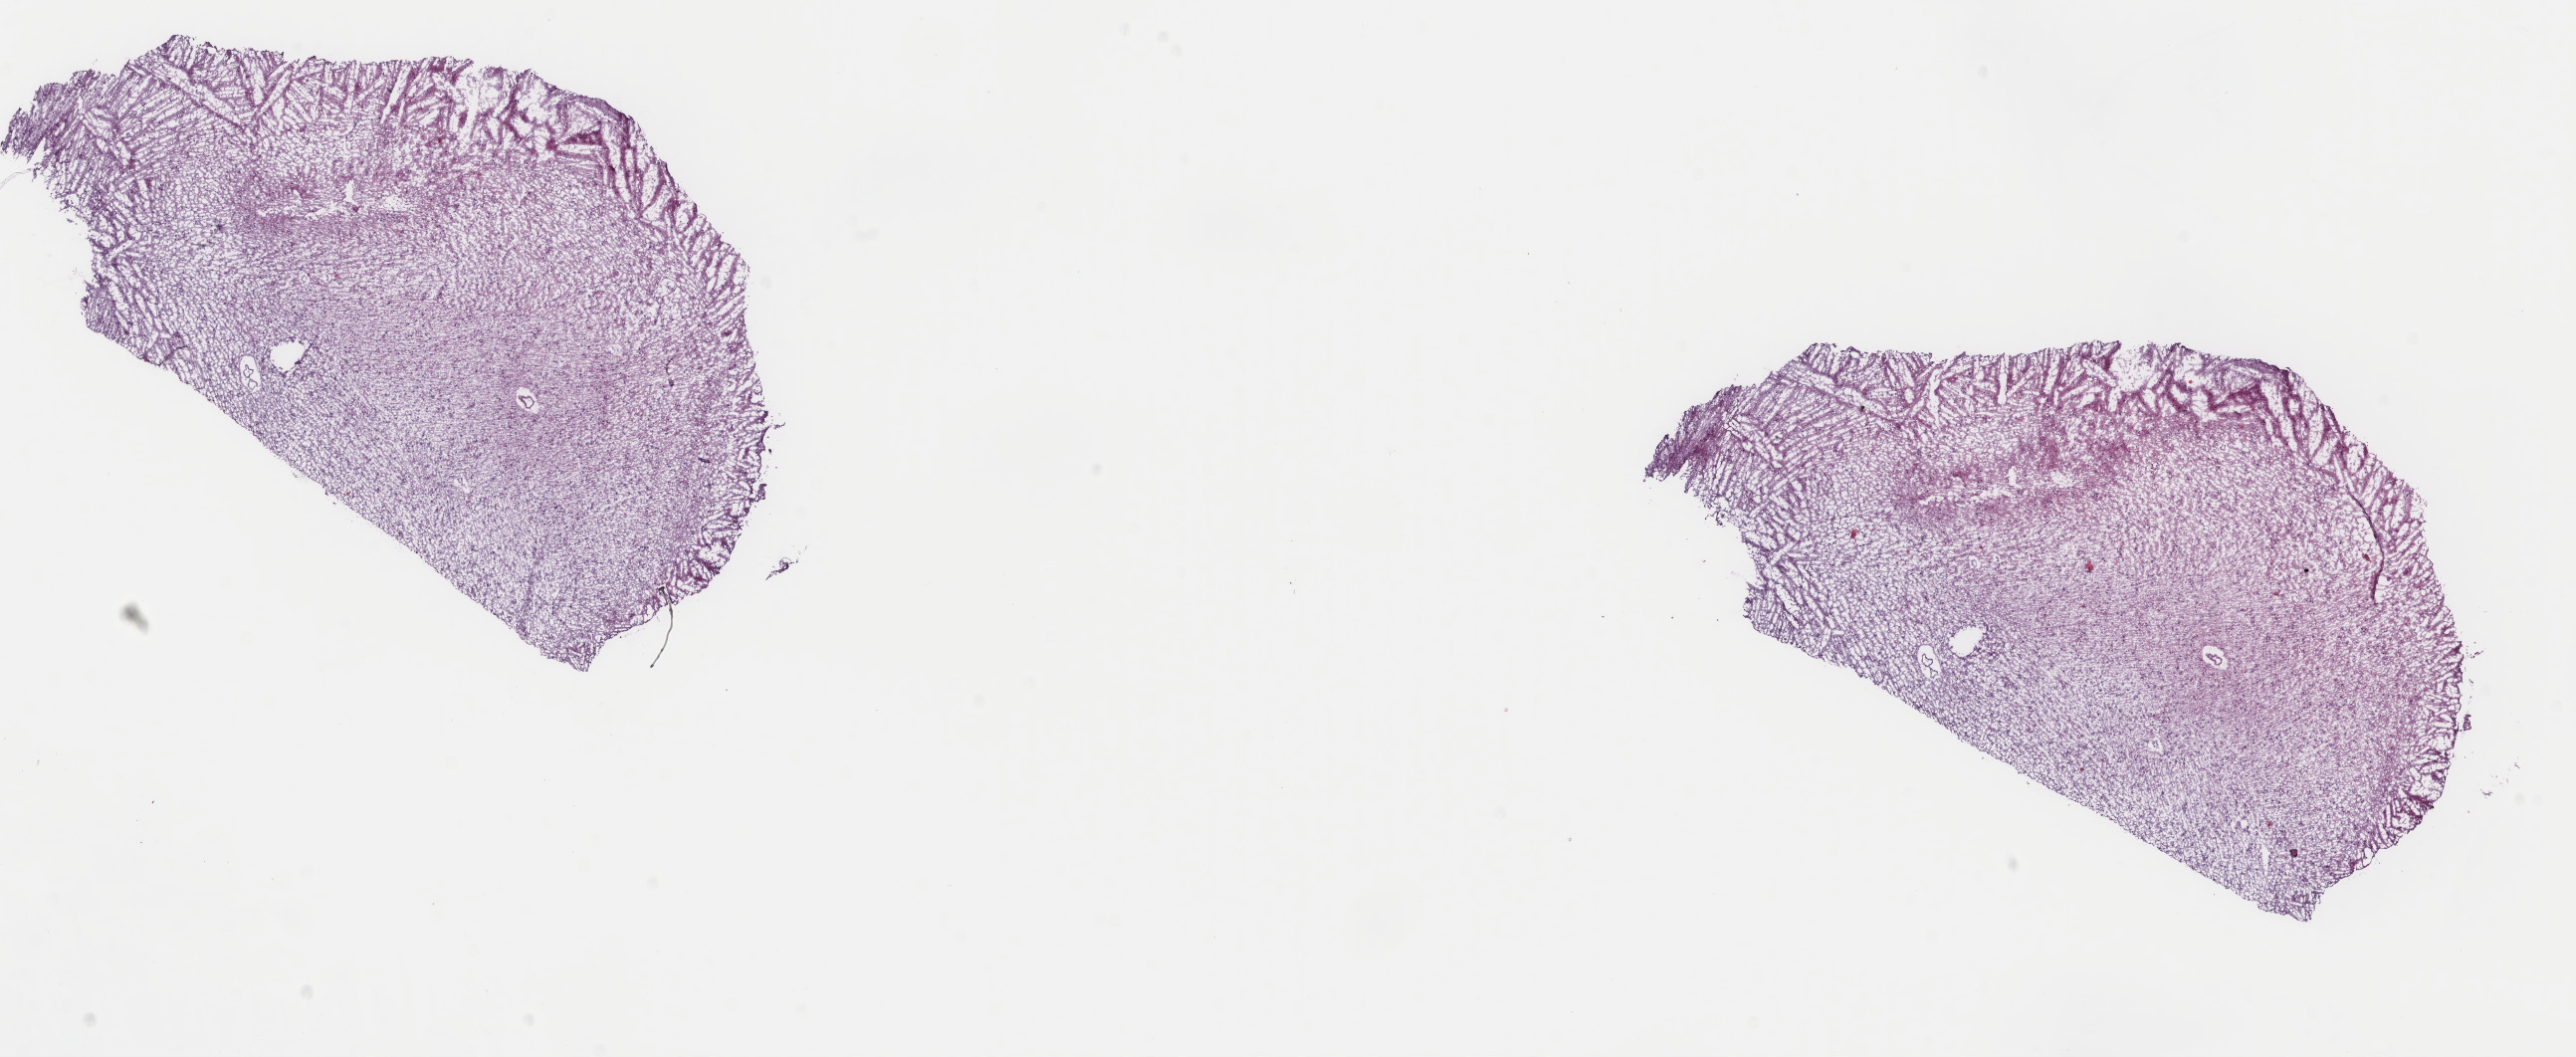
Whole-slide histology image, Hematoxylin and eosin (H&E) stained — low-resolution overview of the scanned area, about 20.5 x 8.4 mm (from a 40x scan), frozen section from the top of the tissue portion, sample: primary tumour, brain. Female, age 34 years at initial diagnosis. Histologic grade: G2 (moderately differentiated). Slide review estimates, as recorded: tumour cells 40%, tumour nuclei 80%, normal cells 5%, stromal cells 55%, necrosis 0%. Inflammatory infiltration, as recorded: lymphocyte infiltration 0%, monocyte infiltration 0%, neutrophil infiltration 0%.
Histologic diagnosis: Astrocytoma, NOS (cerebrum).